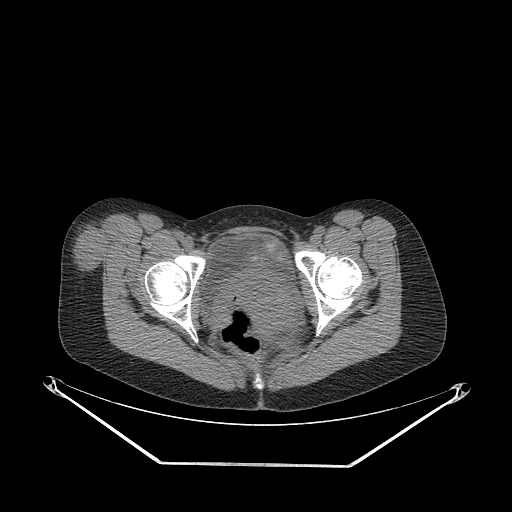
CT of an extremity soft-tissue mass (from a PET/CT study), one axial slice. Slice 67 of 267 in the series (ordered by position). Reconstruction kernel STANDARD. Soft-tissue window (W 400 / L 40 HU). 3.75 mm slice thickness. 512 × 512 image matrix. Female patient. From the clinical record (not read from this slice): histological type: synovial sarcoma; grade: intermediate; site of the primary tumour: right thigh.
Outlined on this slice (expert contour drawn on MRI and transferred to this co-registered scan by the dataset authors):
- gross tumour volume including surrounding oedema: bounding box <71,221,120,275> (left, top, right, bottom; pixels)
- gross tumour volume (mass): <73,221,120,273>